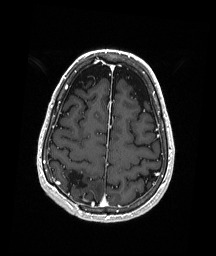
Brain MRI from a brain-tumour surgery series, one axial slice; T1-weighted post-contrast; 1 mm slice thickness; 216 × 256 image matrix, field of view 211 × 250 mm. From the clinical record (not read from this slice): histopathology: Astrocytoma; WHO grade: 3; IDH mutation: yes.
Annotated regions visible in this slice (outlined manually by an expert reader):
- previous resection cavity: bounding box (x1, y1, x2, y2) in pixels: (66, 171, 88, 195)